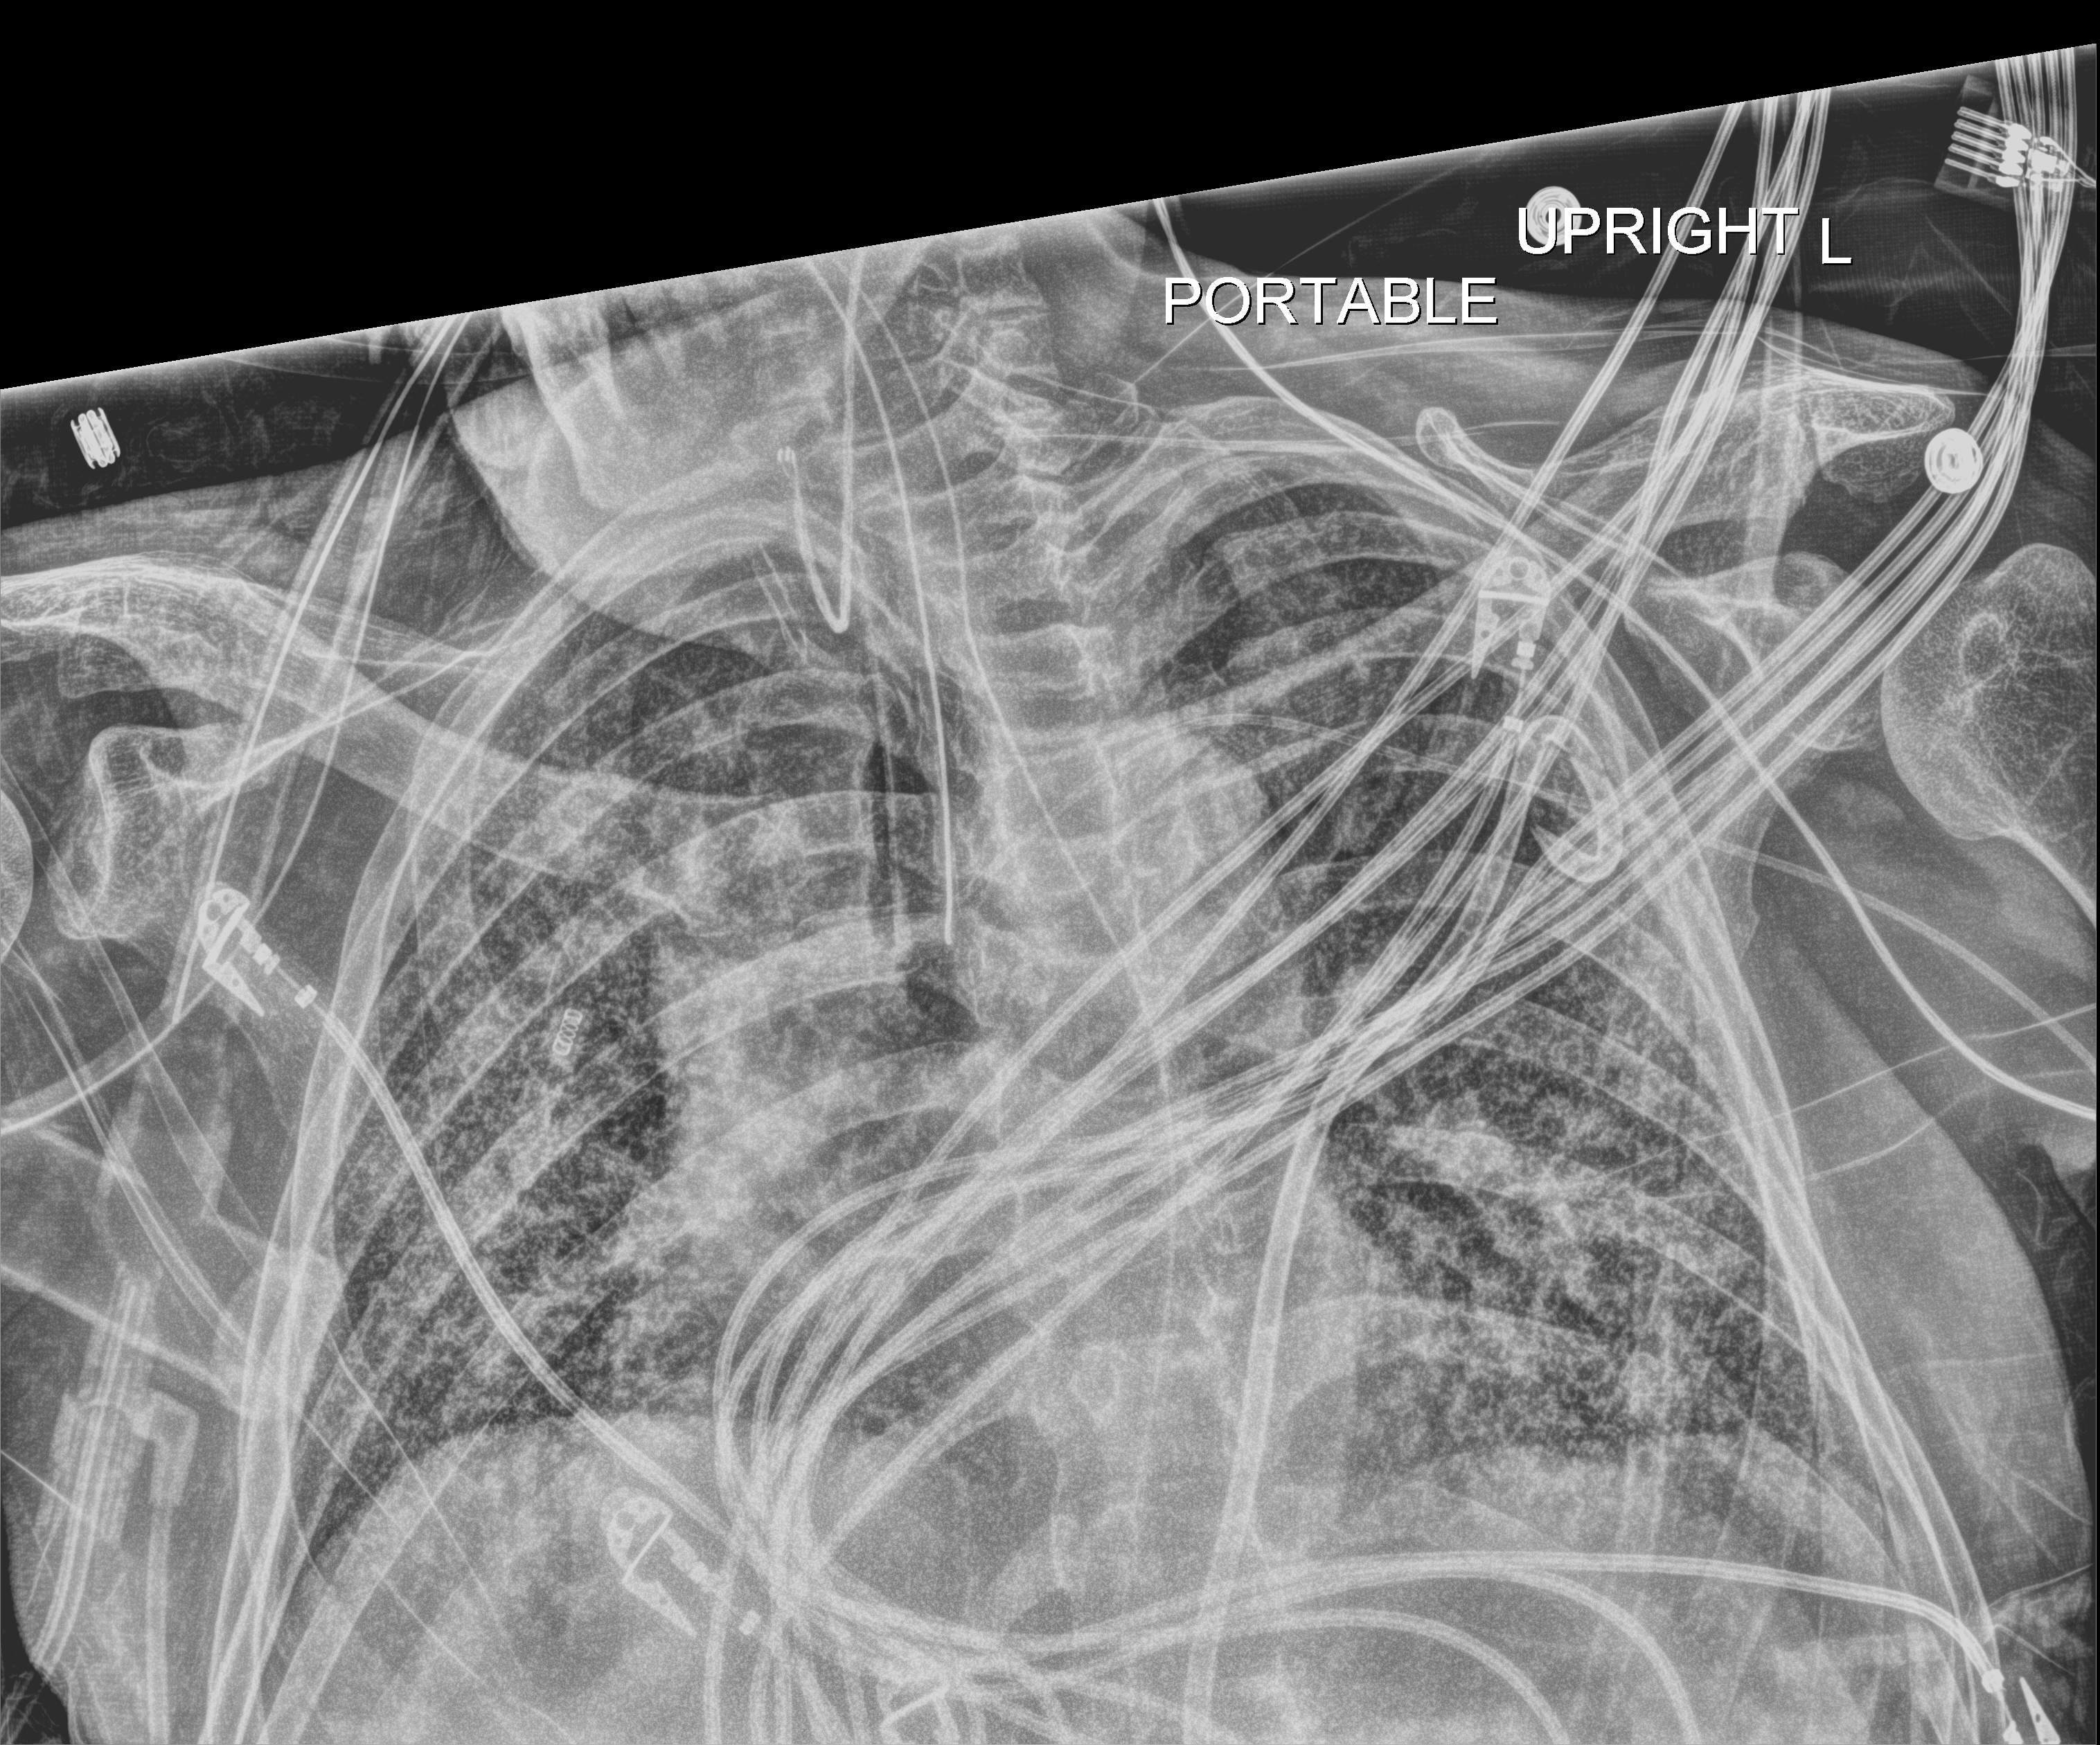
Chest radiograph (digital radiography), anteroposterior (AP) projection. Patient hospitalised with COVID-19; male, aged 60–74 years.
Admission-level facts for this patient (not findings on this image; timing relative to this image not recorded): length of hospital stay: 54 days.